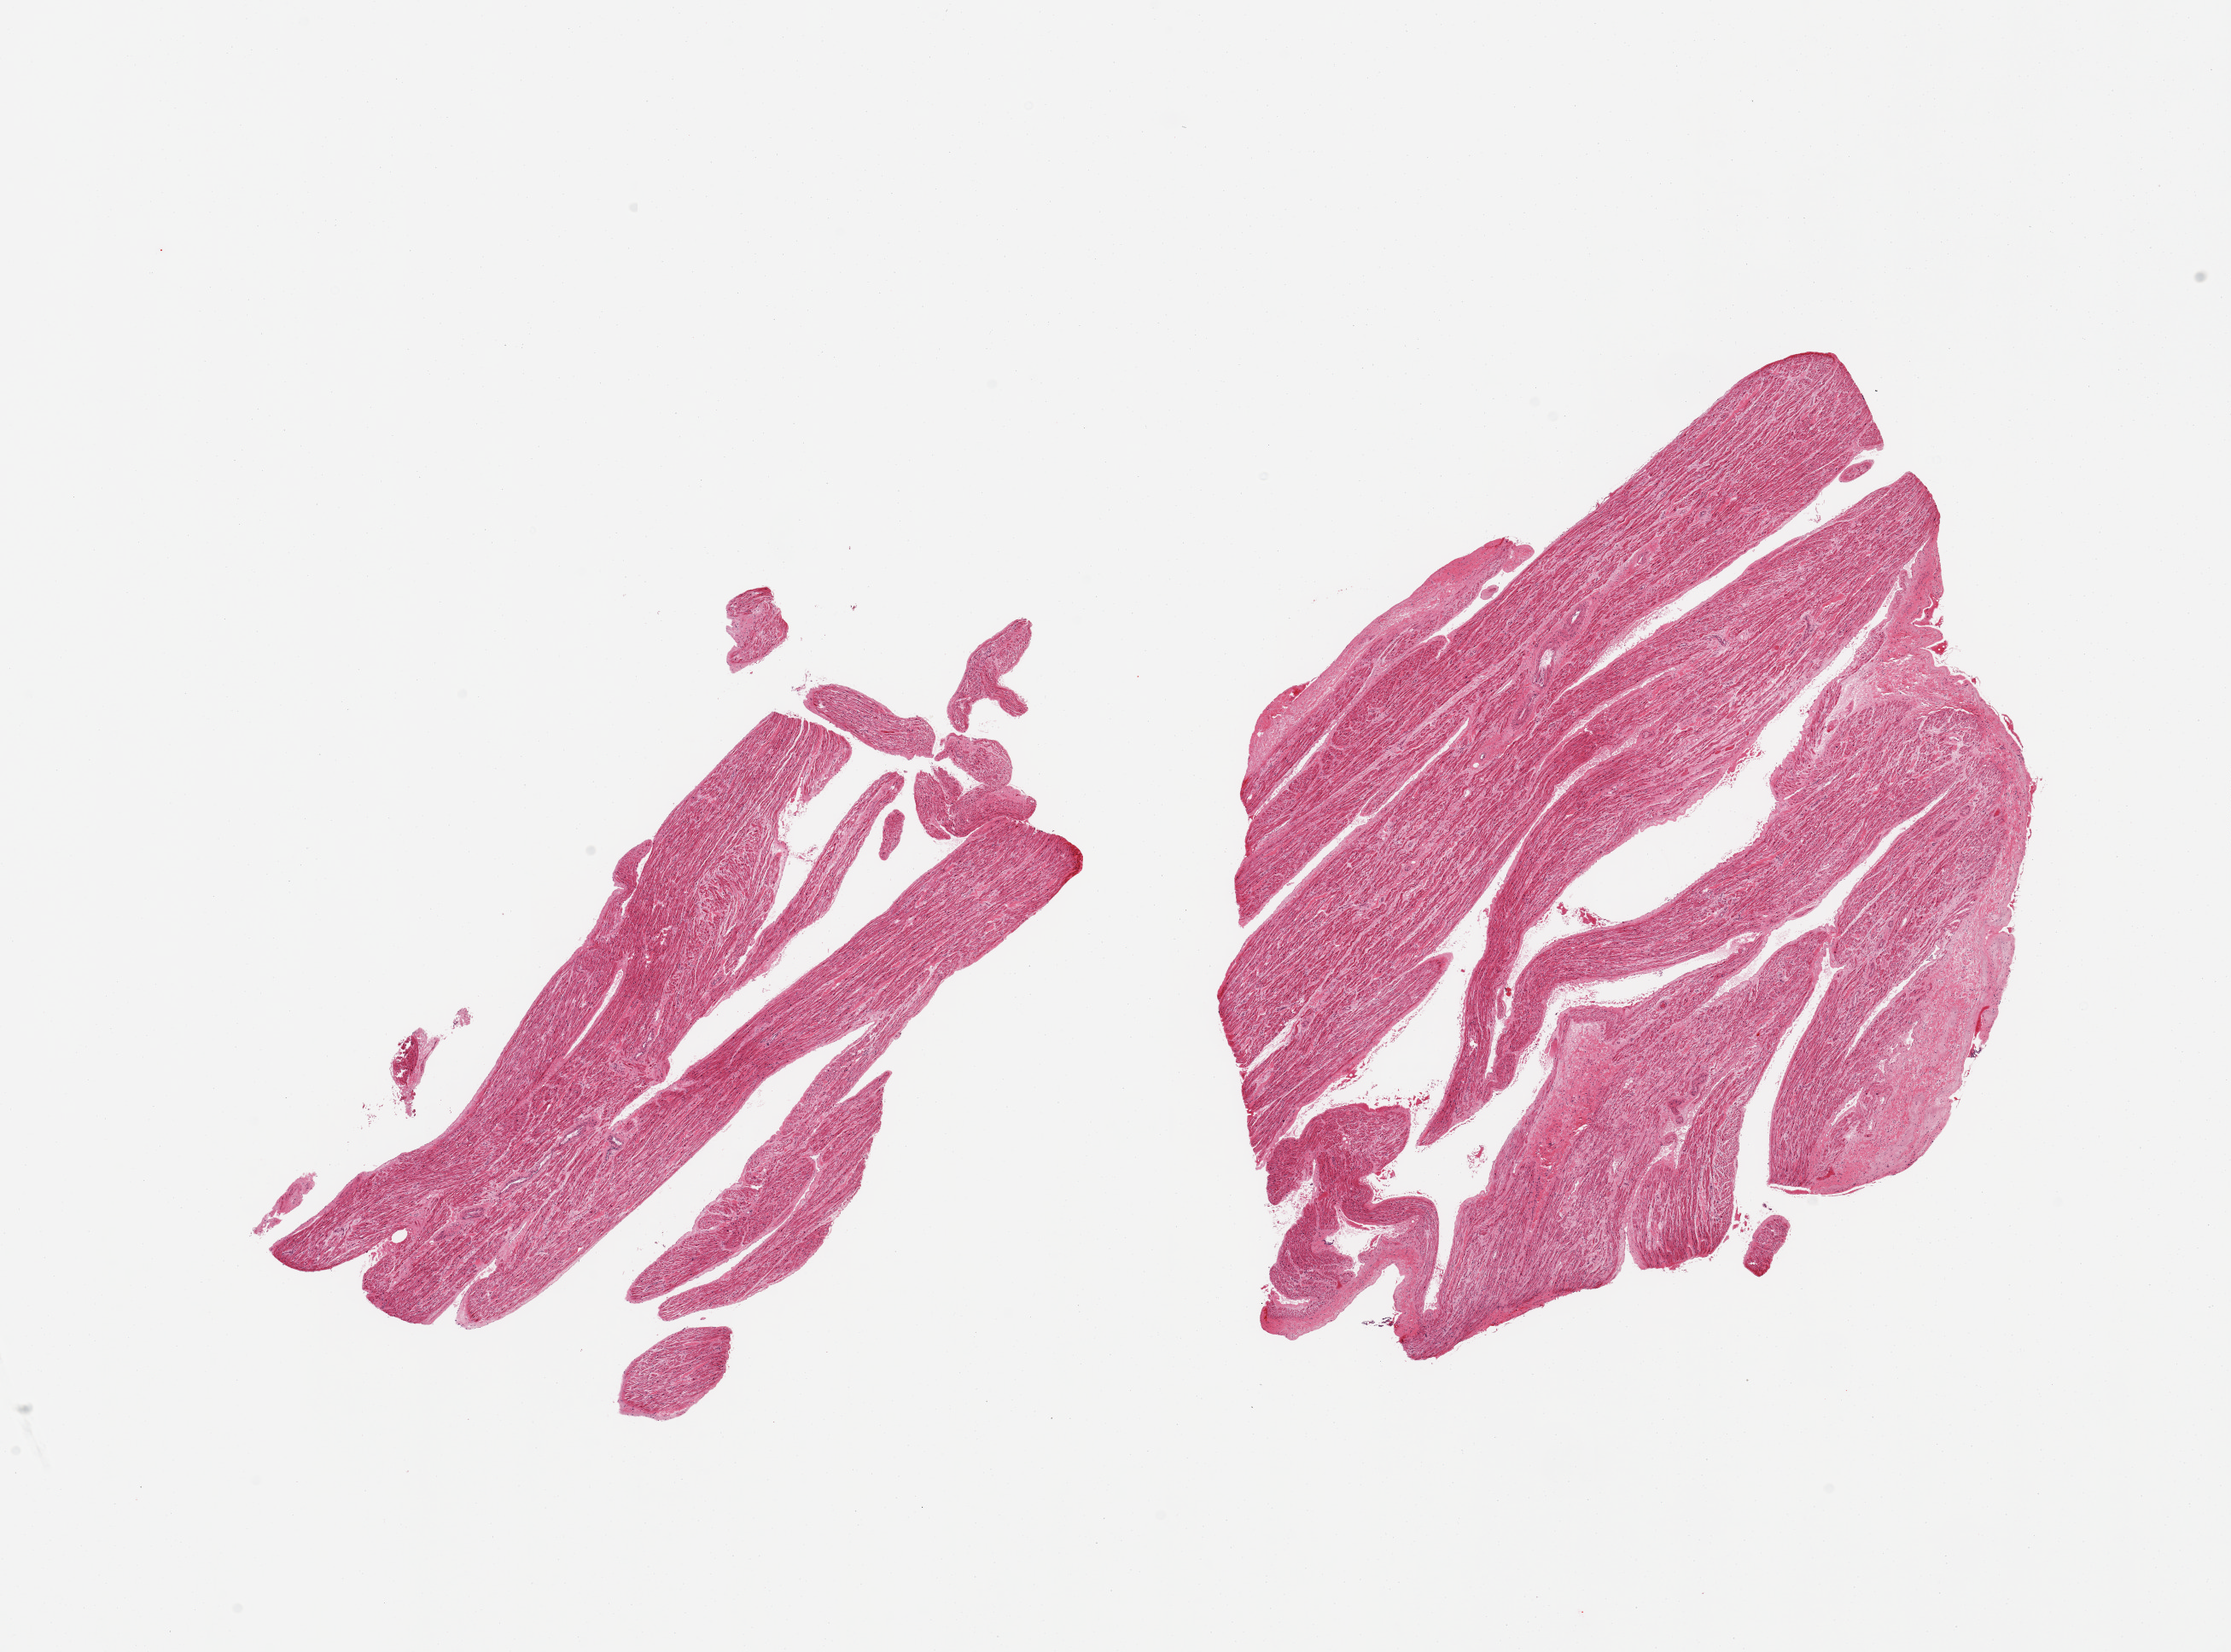
Digitized haematoxylin and eosin-stained section — a low-resolution overview of the entire scanned area, about 20.7 x 15.3 mm (acquisition: 20x scan). PAXgene-fixed paraffin-embedded (PFPE) section. Sampled site (target tissue): auricular appendage. Donor tissue sample.
• pathologist's review note for this sample: 2 pieces